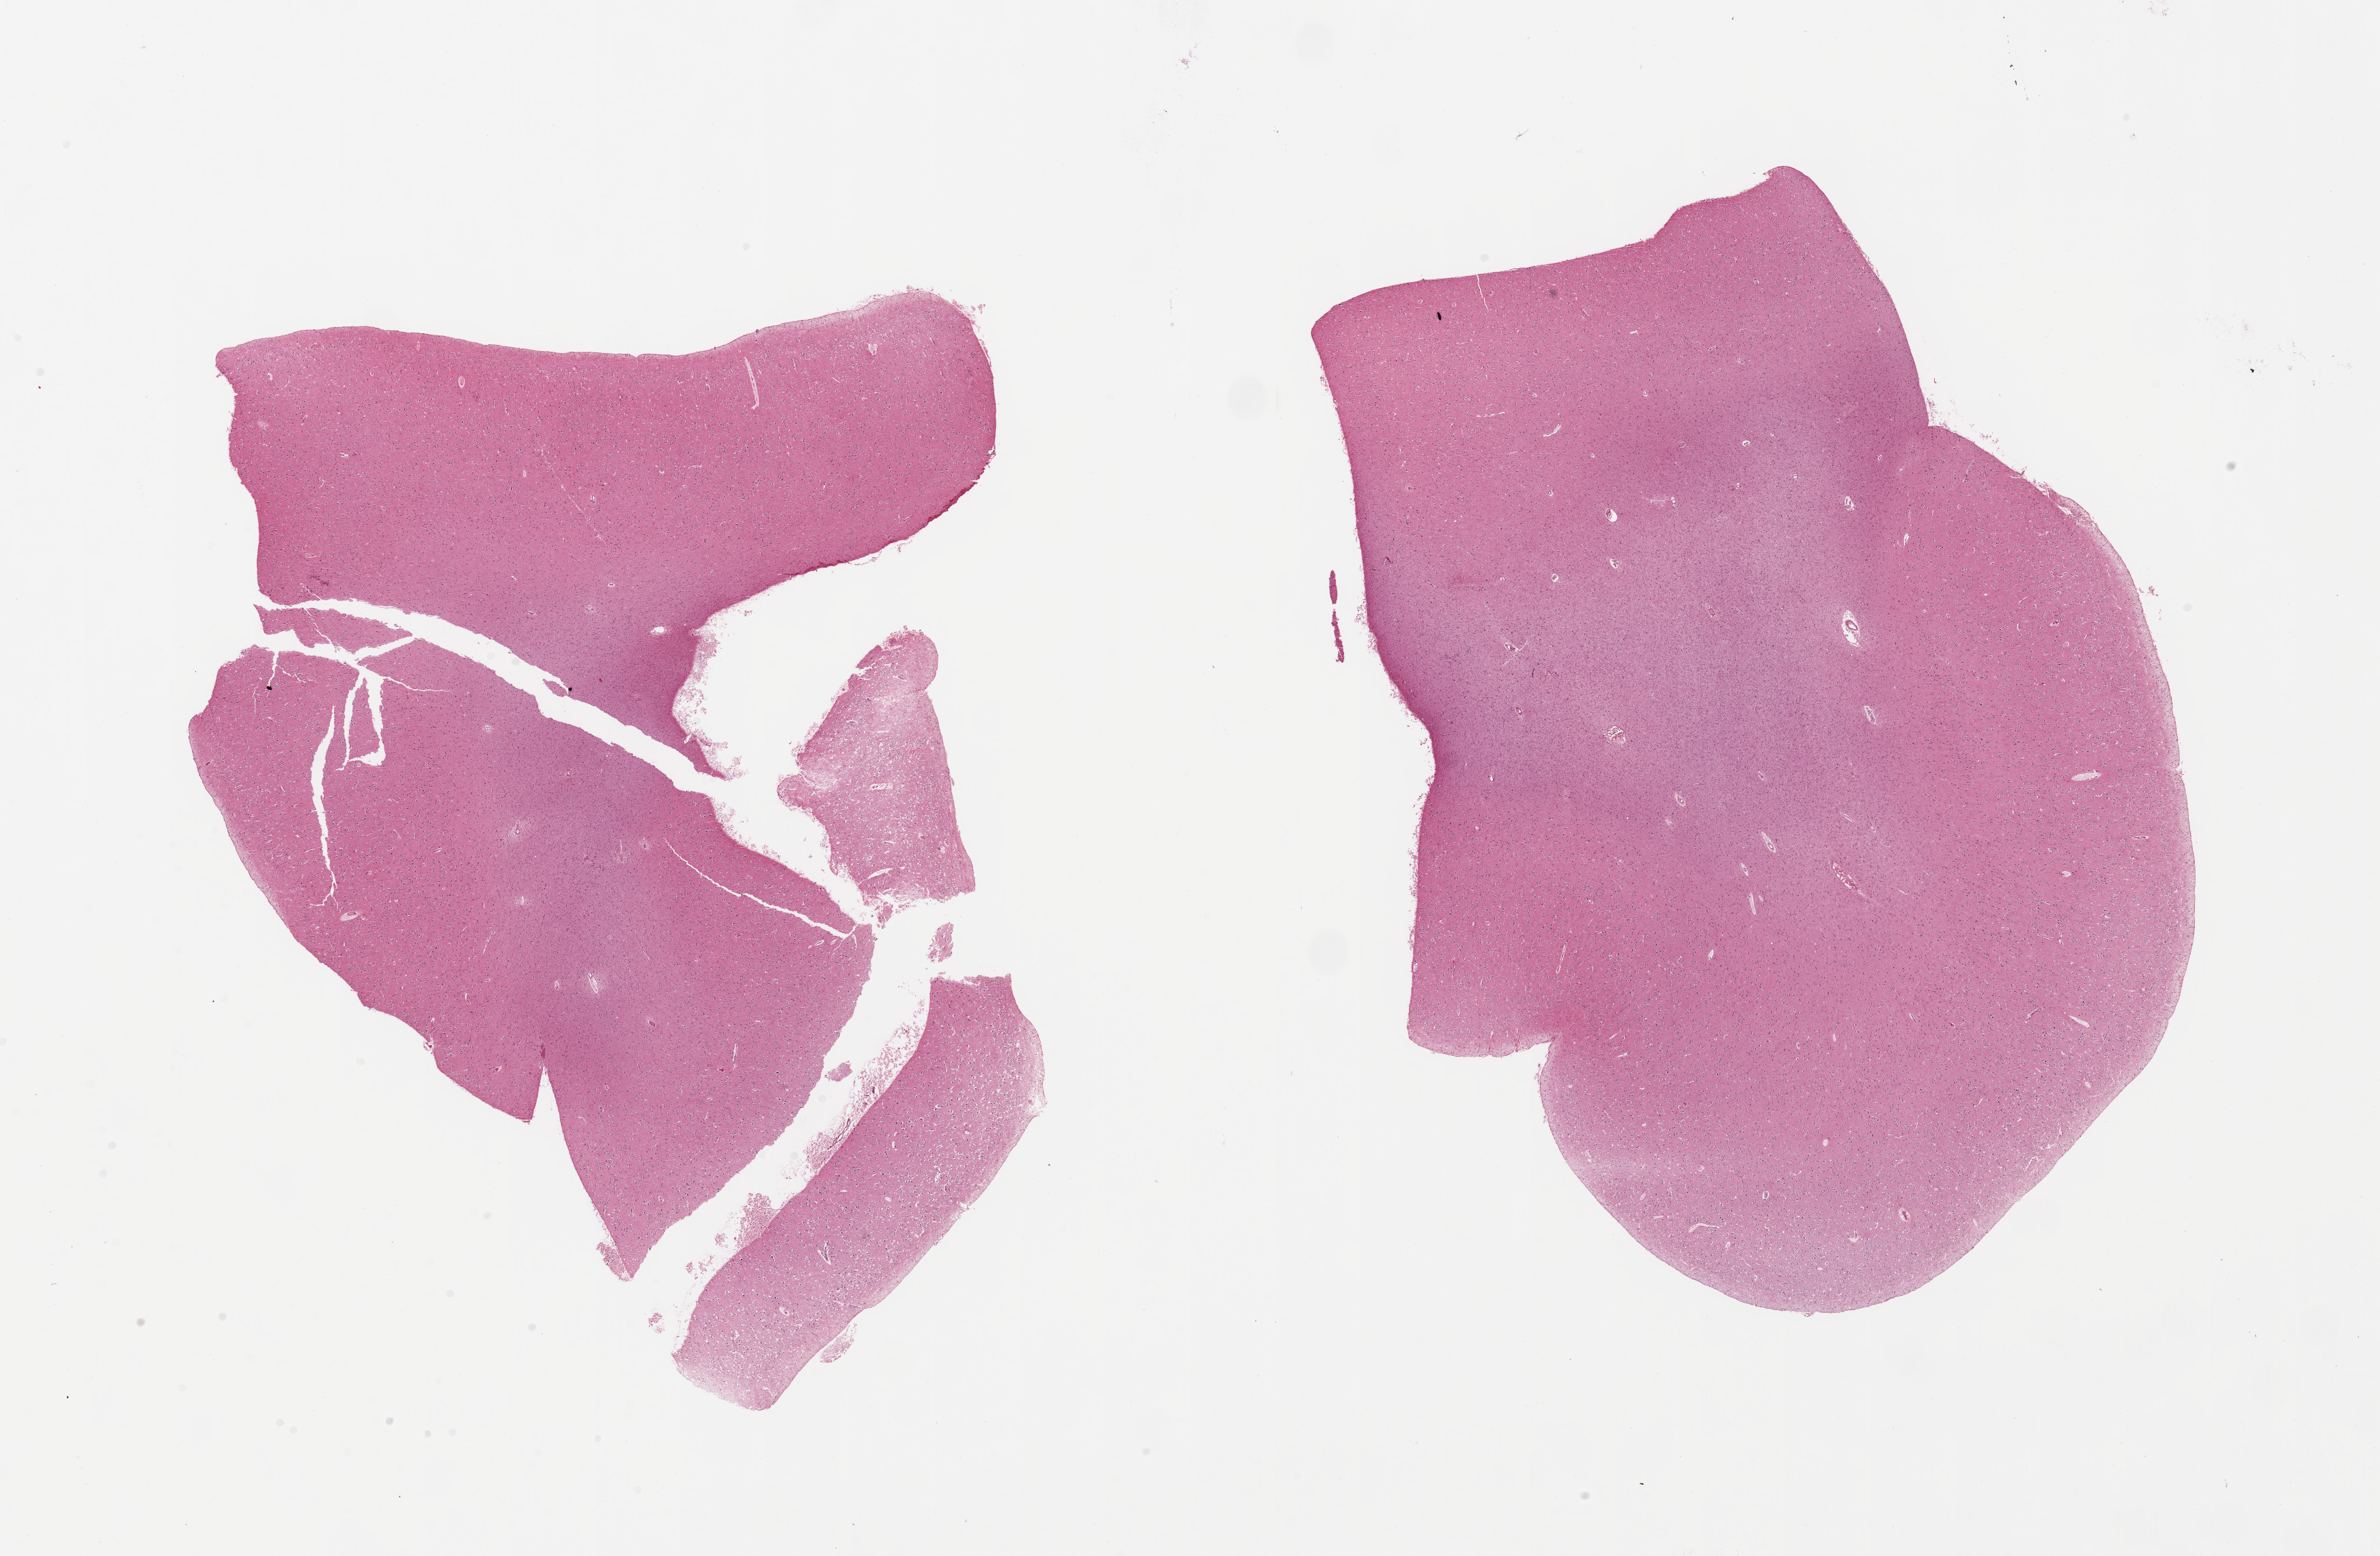
Whole-slide image, hematoxylin and eosin (H&E) stain — low-resolution overview of the scanned area, about 27.6 x 18.0 mm. PAXgene-fixed, paraffin-embedded tissue. Target tissue: cerebellum. Tissue donor sample. Male donor.
Reviewer comment on this tissue sample: 2 pieces; cortex, not cerebellum.